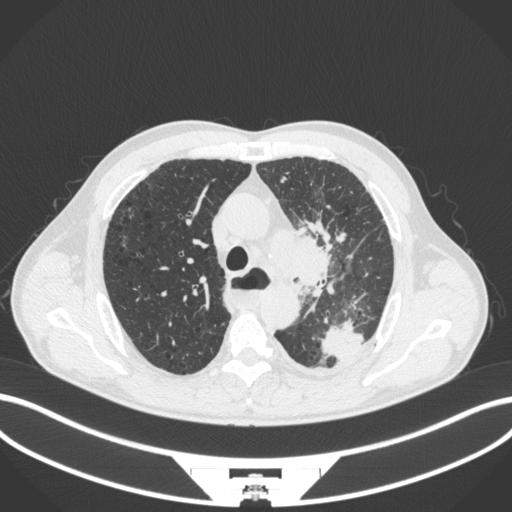
Chest CT, one axial slice; position 277 of 411 along the scan axis; reconstruction kernel B31f; lung window (W 1500 / L -600 HU); 512 × 512 image matrix, field of view 400 × 400 mm. Patient: male, 57 years. Case-level facts recorded for this patient, not image findings: clinical TNM (as recorded): T2a N1 M0.
Annotated regions visible in this slice (bounding box drawn by a radiologist):
- lung tumour (recorded histology: squamous cell carcinoma): bounding box <268,229,346,296> (left, top, right, bottom; pixels)